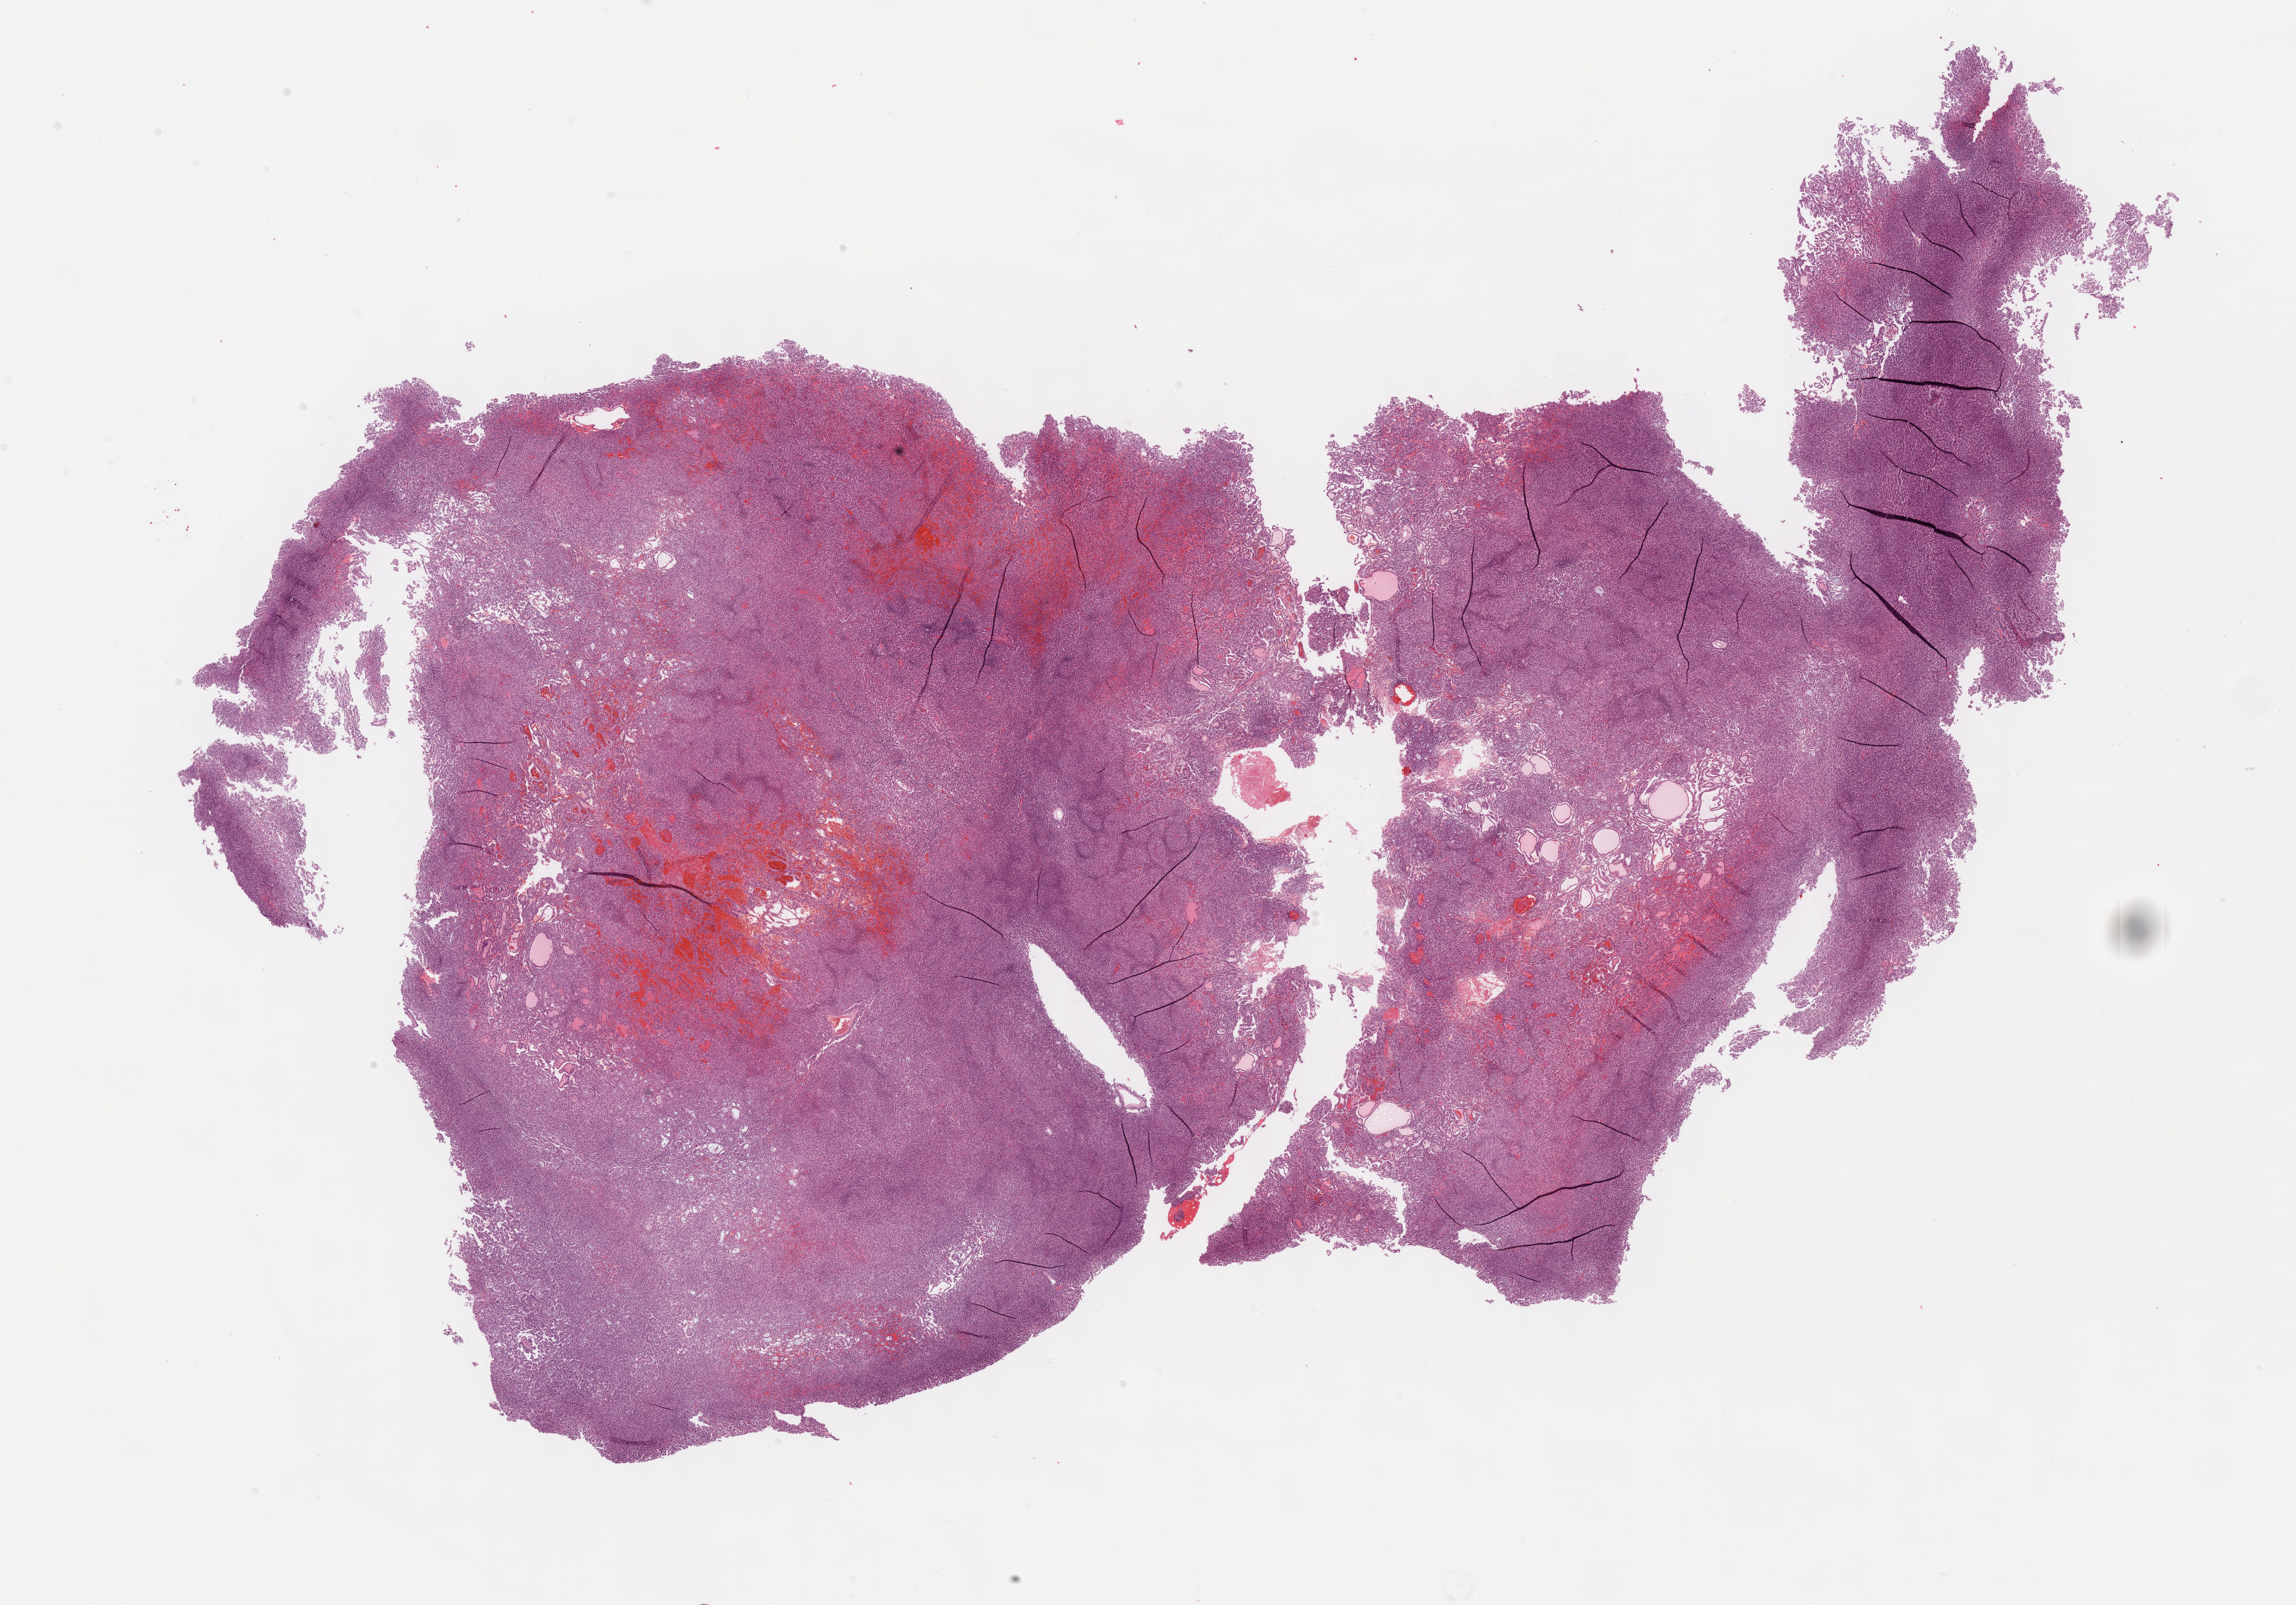
Whole-slide histology image, H&E, a low-resolution overview of the entire scanned area, about 26.2 x 18.3 mm; FFPE section; primary tumour sample from the kidney. Male, age 78 years at initial diagnosis.
TNM: T1a NX MX. Histologic diagnosis: Papillary adenocarcinoma, NOS. AJCC pathologic stage: I.